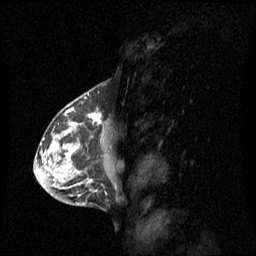
Breast MRI (dynamic contrast-enhanced), one sagittal slice. Position 37 of 60 along the scan axis. Dynamic contrast-enhanced series, image 2 of 3 at this slice position (ordered by acquisition). 1.5 T. TE 4.2 ms, TR 8.4 ms. 2 mm slice thickness. 256 × 256 image matrix. Female patient, age 42 years. Case-level facts recorded for this patient, not image findings: setting: breast cancer imaged before/during neoadjuvant chemotherapy; receptor status: HR-positive, HER2-negative.
Structures marked on this image (semi-automatic segmentation, software-assisted and operator-edited):
- analysis volume of interest (the breast-tissue region the enhancement analysis was run in; not a lesion): box from (x=56, y=113) to (x=119, y=185) px
- tumour enhancement mask (voxels above the 70 % enhancement threshold inside the analysis volume of interest): (x=66, y=114)–(x=101, y=157)